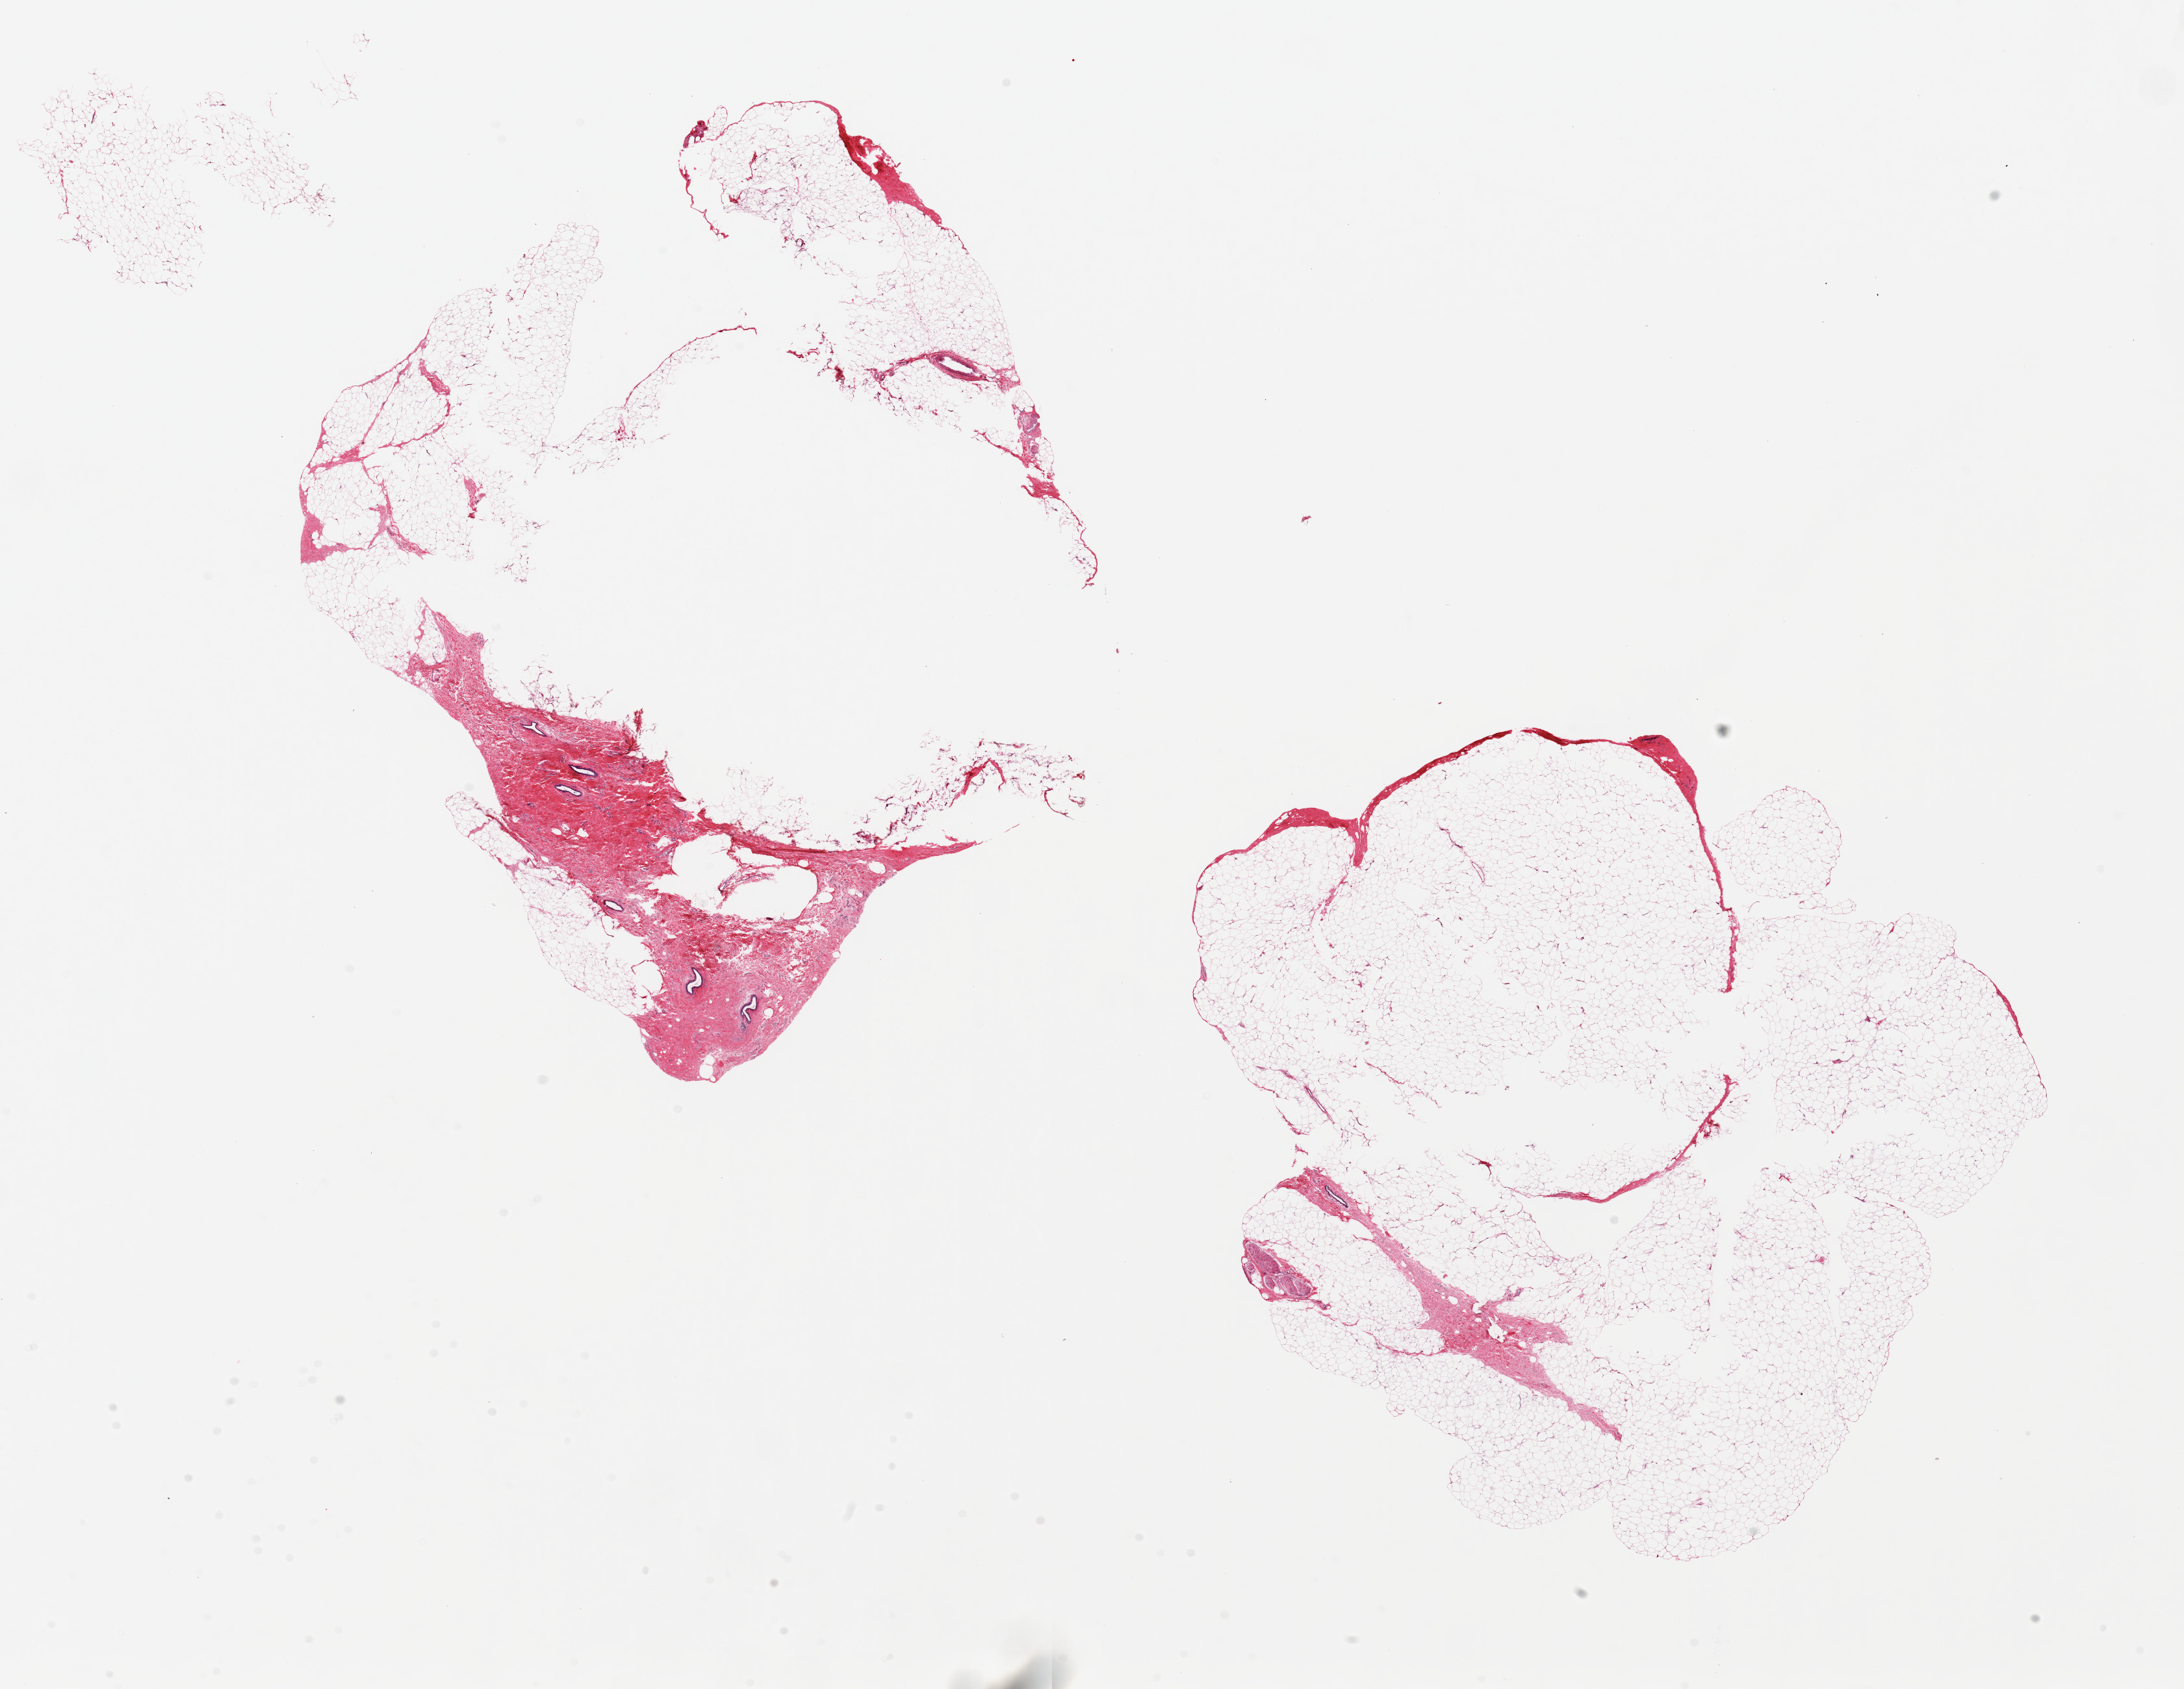
H&E whole-slide image, brightfield — whole scanned area (about 26.6 x 20.6 mm, from a 20x scan) shown as a low-resolution overview, PAXgene-fixed paraffin-embedded (PFPE) section, sampled site (target tissue): breast, tissue donor sample. Donor sex: male.
Pathologist's review note for this sample: 2 pieces, 9.5x9 & 10x9mm; several ducts in fibrous tissue; 80-90% adipose with central unfixed holes.